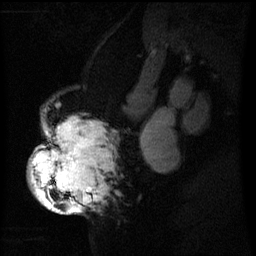
Breast MRI (dynamic contrast-enhanced), one sagittal slice. Position 35 of 60 along the scan axis. Dynamic contrast-enhanced series, image 2 of 3 at this slice position (ordered by acquisition). 1.5 T. TE 4.2 ms, TR 8 ms. 2.2 mm slice thickness. 256 × 256 image matrix, field of view 200 × 200 mm. Female patient, age 50 years.
Structures marked on this image (semi-automatically segmented with operator editing):
- analysis volume of interest (the breast-tissue region the enhancement analysis was run in; not a lesion): bounding box <31,112,111,211> (left, top, right, bottom; pixels)
- tumour enhancement mask (voxels above the 70 % enhancement threshold inside the analysis volume of interest): <32,120,103,211>